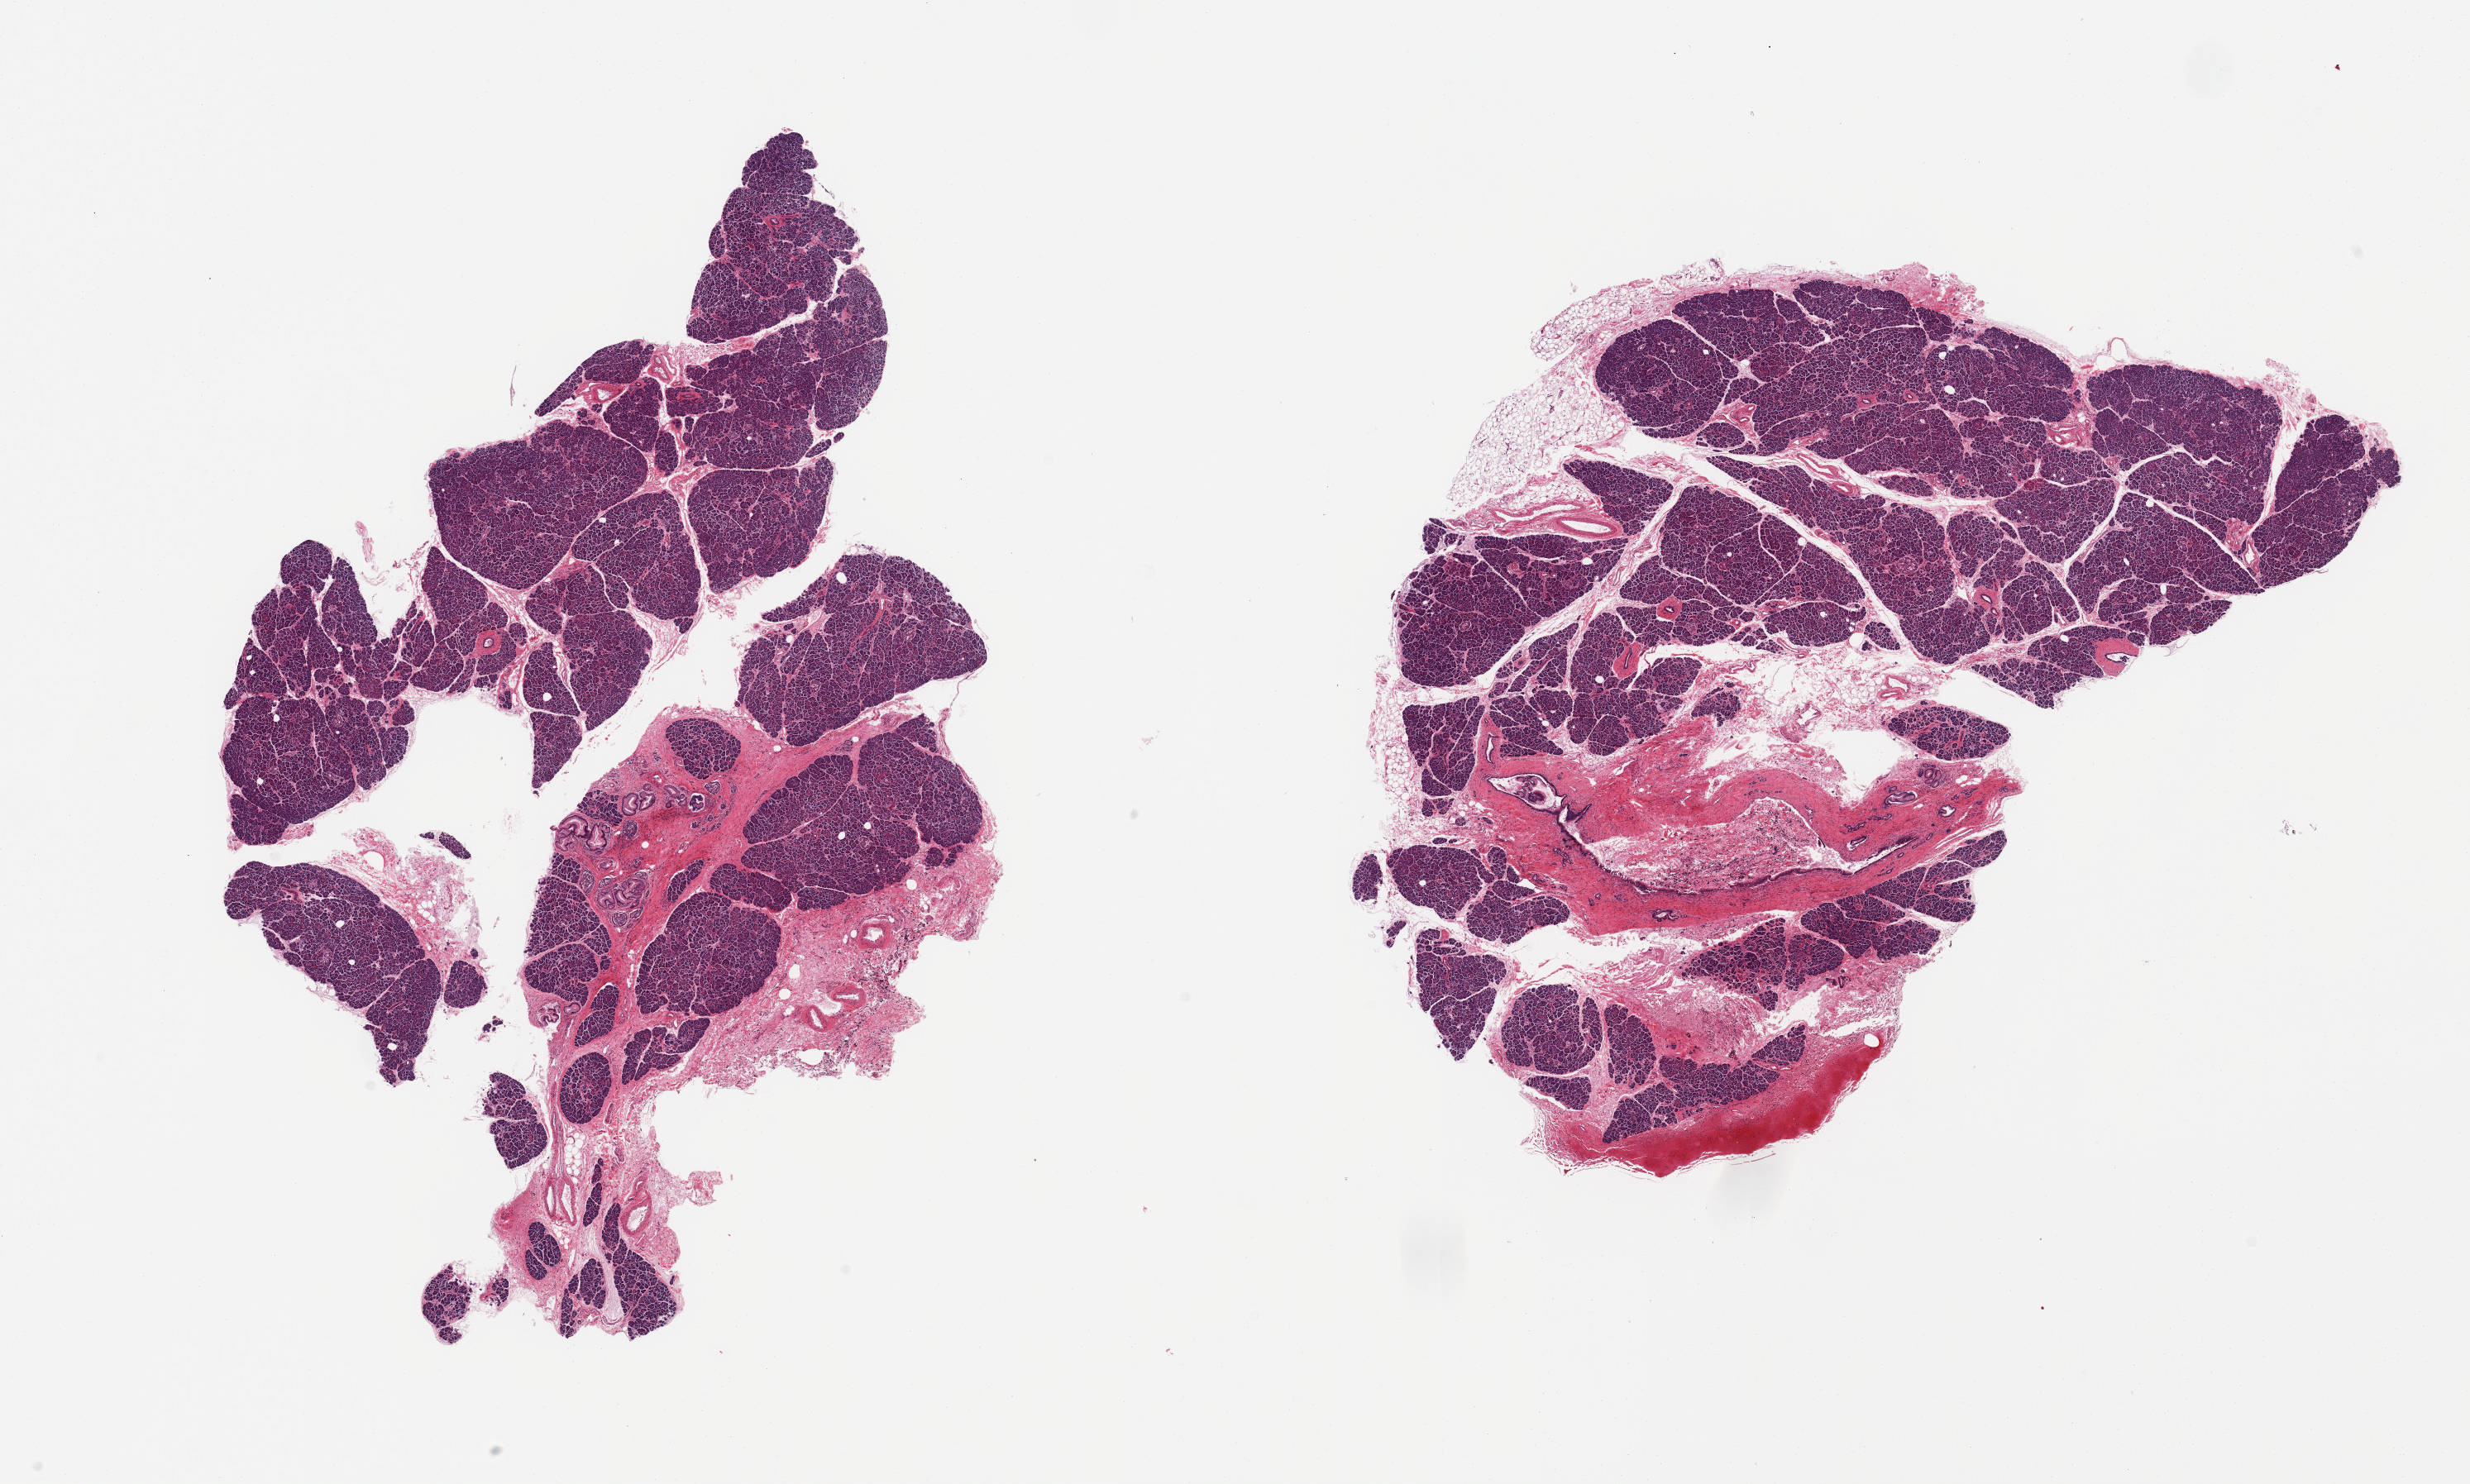
Digitized haematoxylin and eosin-stained section — a low-resolution overview of the entire scanned area, about 23.6 x 14.2 mm (slide scanned at 20x). PAXgene-fixed, paraffin-embedded tissue. Section of pancreas (target tissue). Donor tissue sample. Donor sex: female.
Review note (as recorded): 2 pieces; small portion of attached fat on 1 piece, focal PanIN-1, some atrophy.